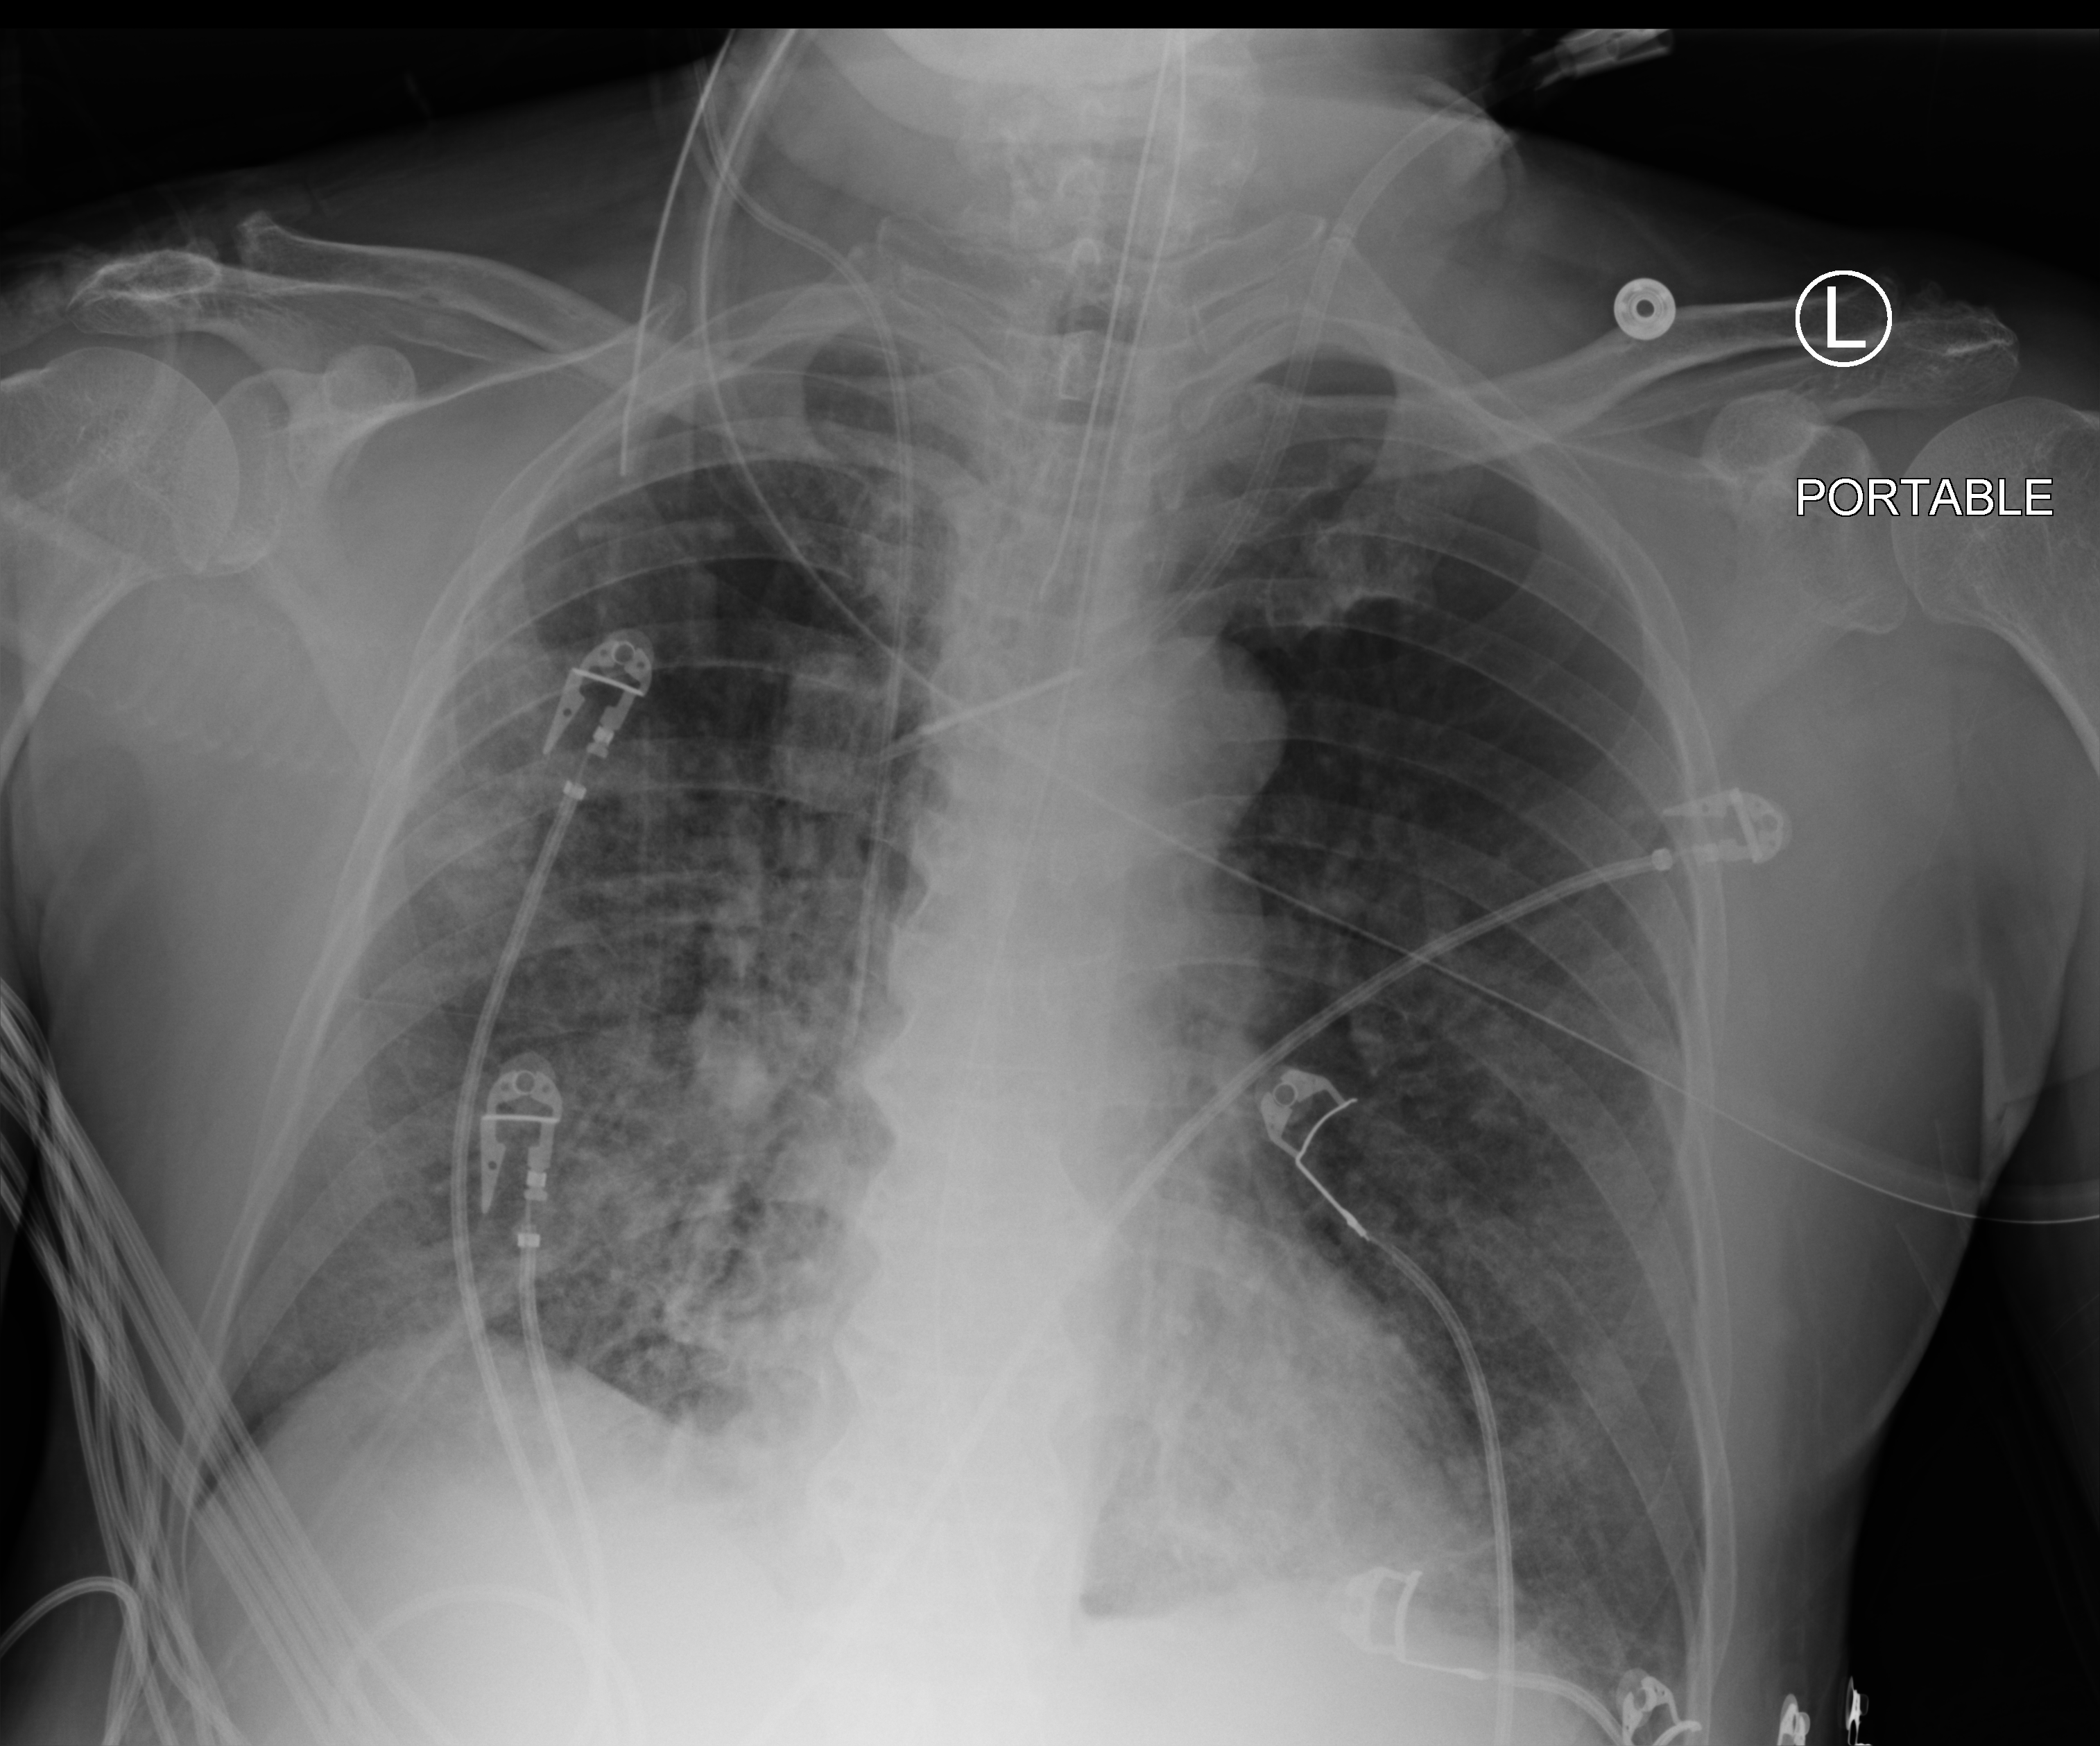
Portable chest radiograph. Male patient hospitalised with COVID-19, age 60–74 years.
Hospital-stay facts (about this admission, not read from this image; timing relative to this image not recorded): admitted to intensive care during this hospital stay: yes; mechanically ventilated during this hospital stay: yes.